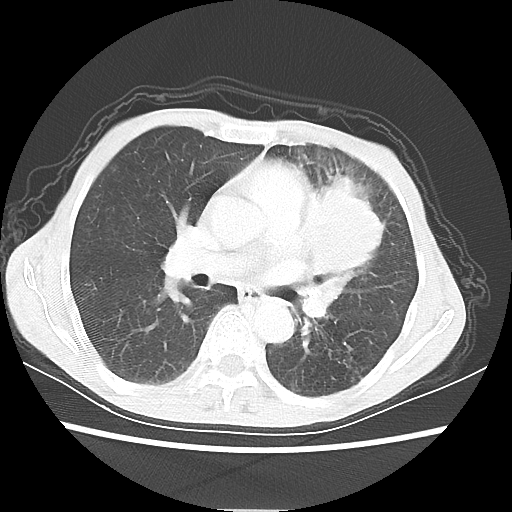
Chest CT, one axial slice. Position 33 of 56 along the scan axis. Reconstruction kernel LUNG. 80 kVp. Lung window (W 1500 / L -600 HU). 512 × 512 image matrix. Patient: female, 60 years. Case-level facts recorded for this patient, not image findings: clinical TNM (as recorded): T4 N1 M0.
Structures marked on this image (rectangle marked by the reading radiologist):
- lung tumour (recorded histology: adenocarcinoma): bounding box <303,177,388,288> (left, top, right, bottom; pixels)